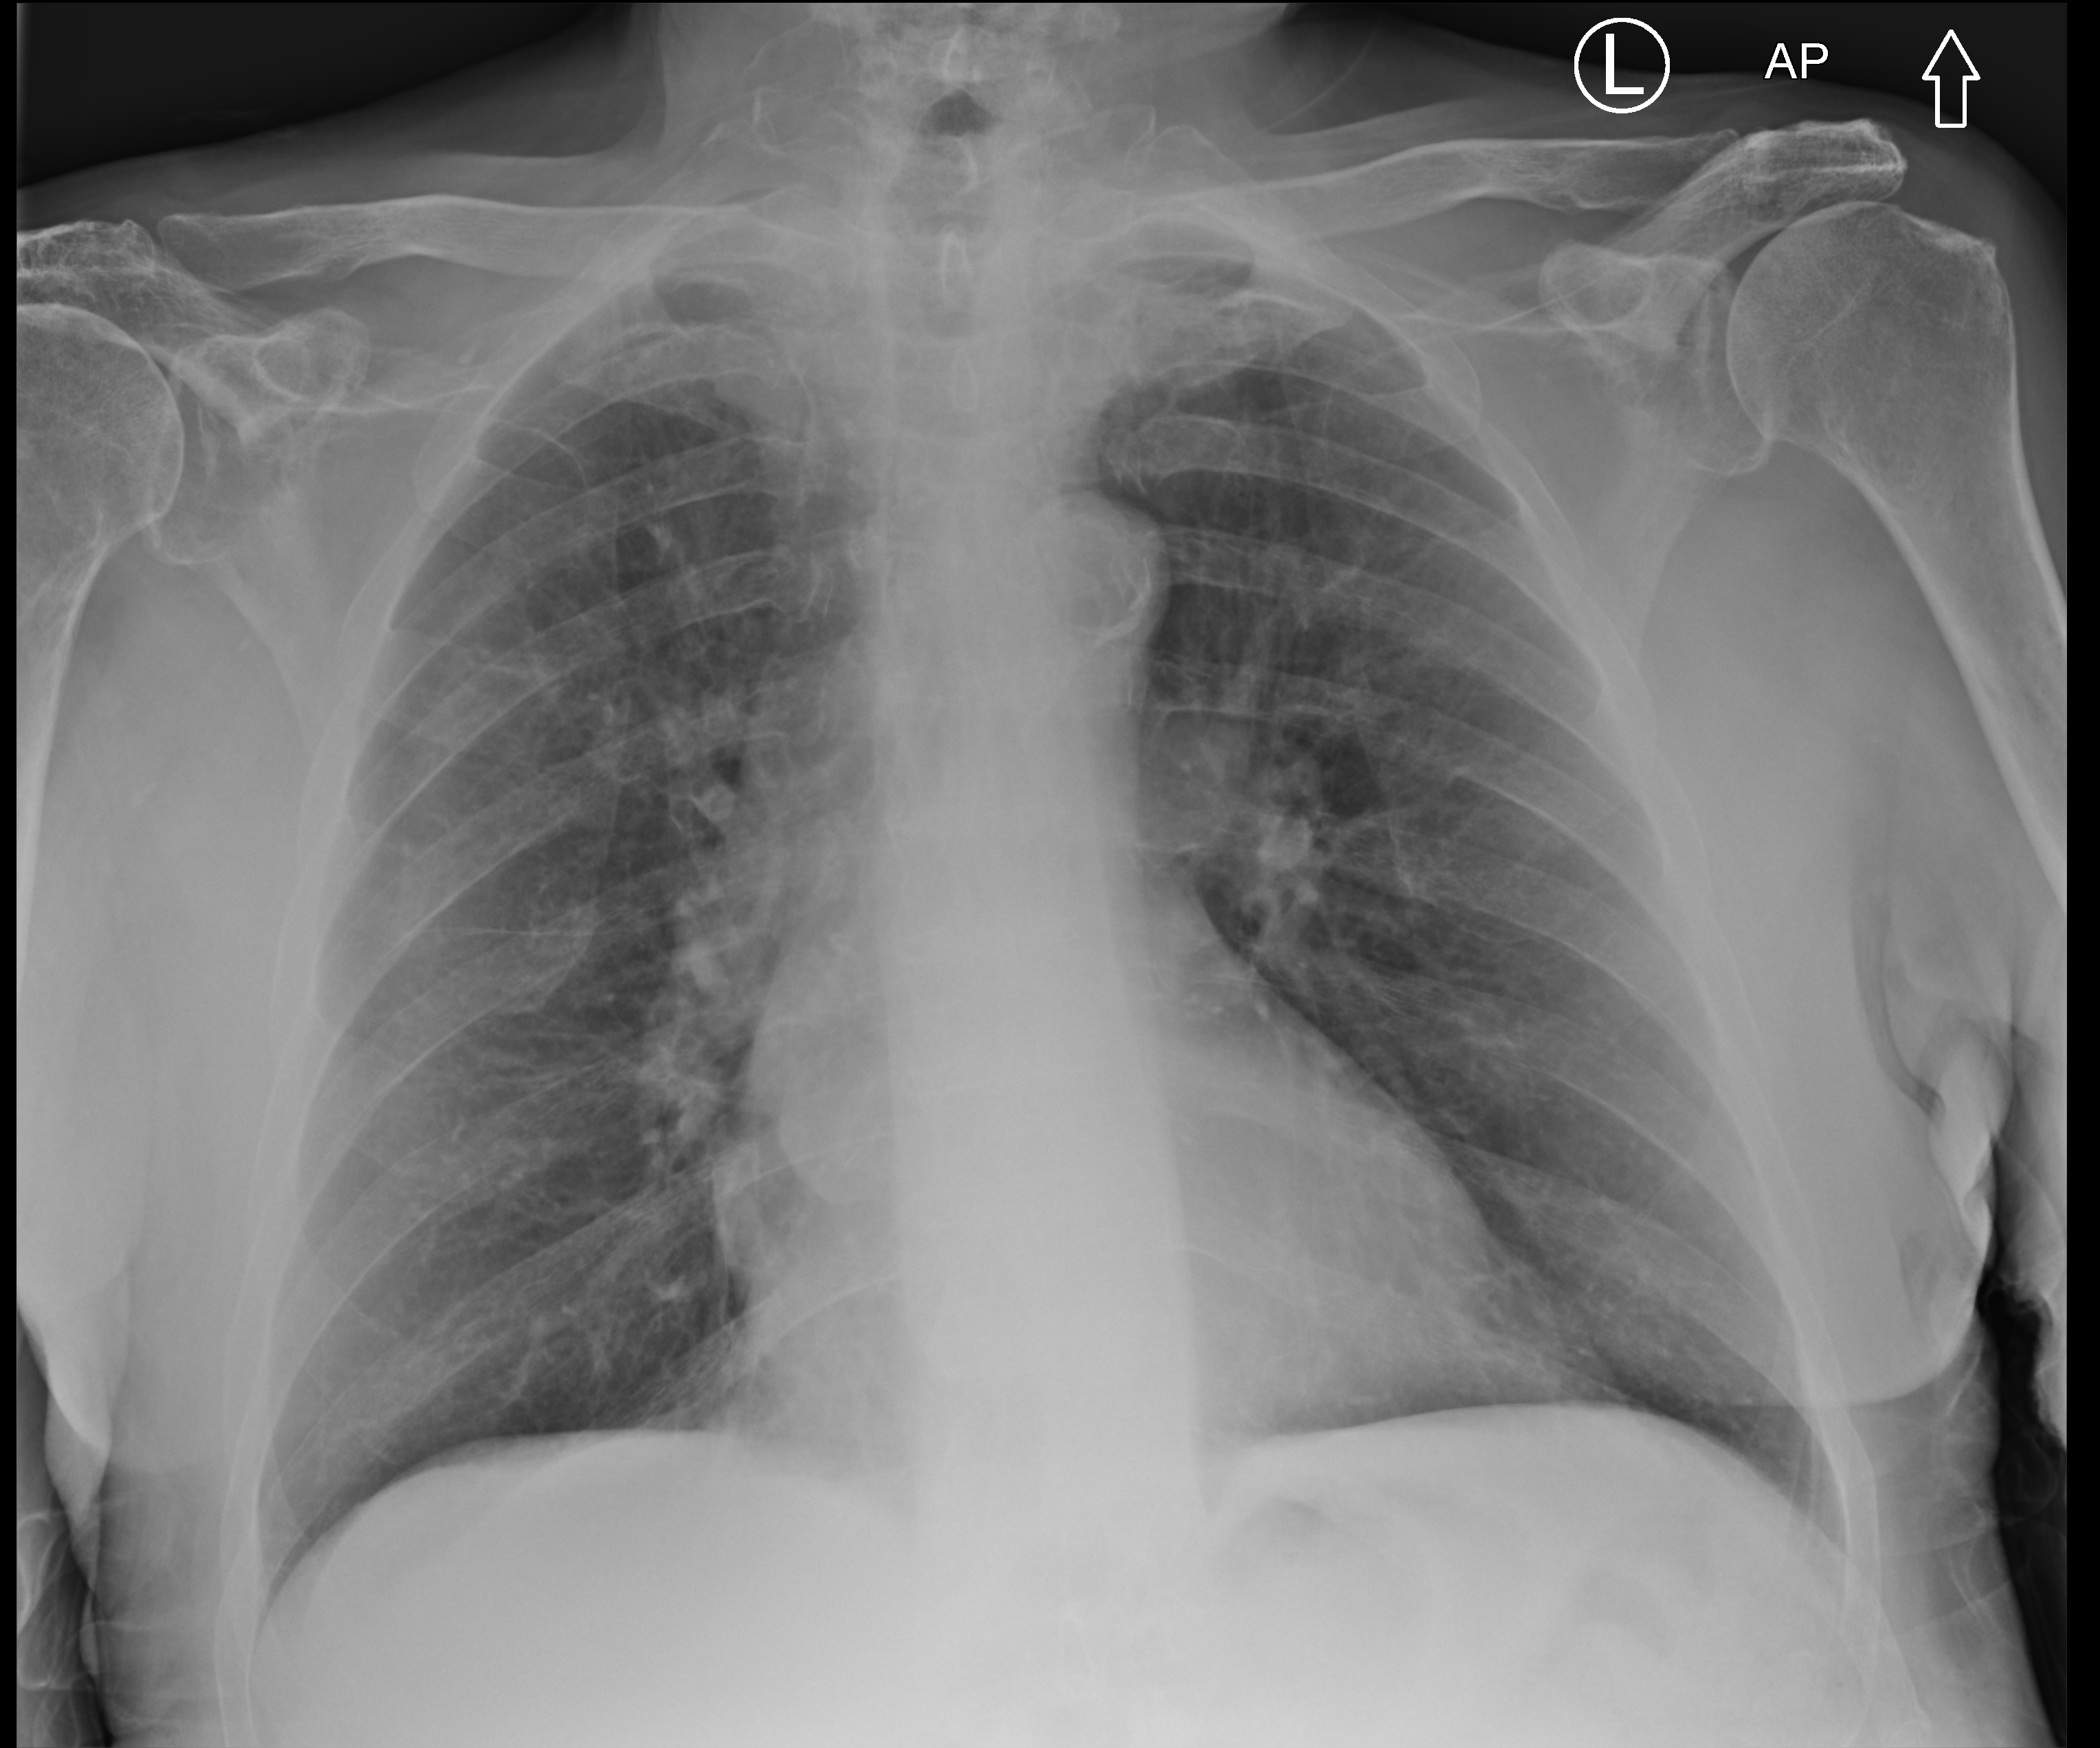
Chest radiograph (computed radiography); anteroposterior (AP) projection. Patient hospitalised with COVID-19; male, aged 75–90 years.
Hospital-stay facts (about this admission, not read from this image; timing relative to this image not recorded): mechanically ventilated during this hospital stay: no; admitted to intensive care during this hospital stay: no.